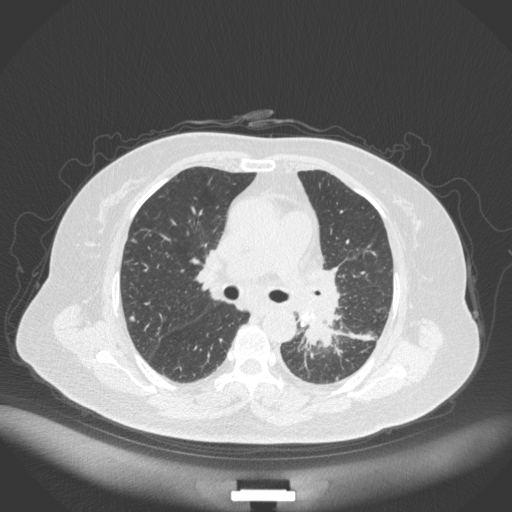
Chest CT, one axial slice. Position 209 of 328 along the scan axis. 120 kVp. Lung window (W 1500 / L -600 HU). 512 × 512 image matrix, field of view 400 × 400 mm. Patient: female, 69 years. From the clinical record (not read from this slice): clinical TNM (as recorded): T2b N3 M1.
Annotated regions visible in this slice (bounding box drawn by a radiologist):
- lung tumour (recorded histology: adenocarcinoma): box from (x=291, y=305) to (x=335, y=353) px